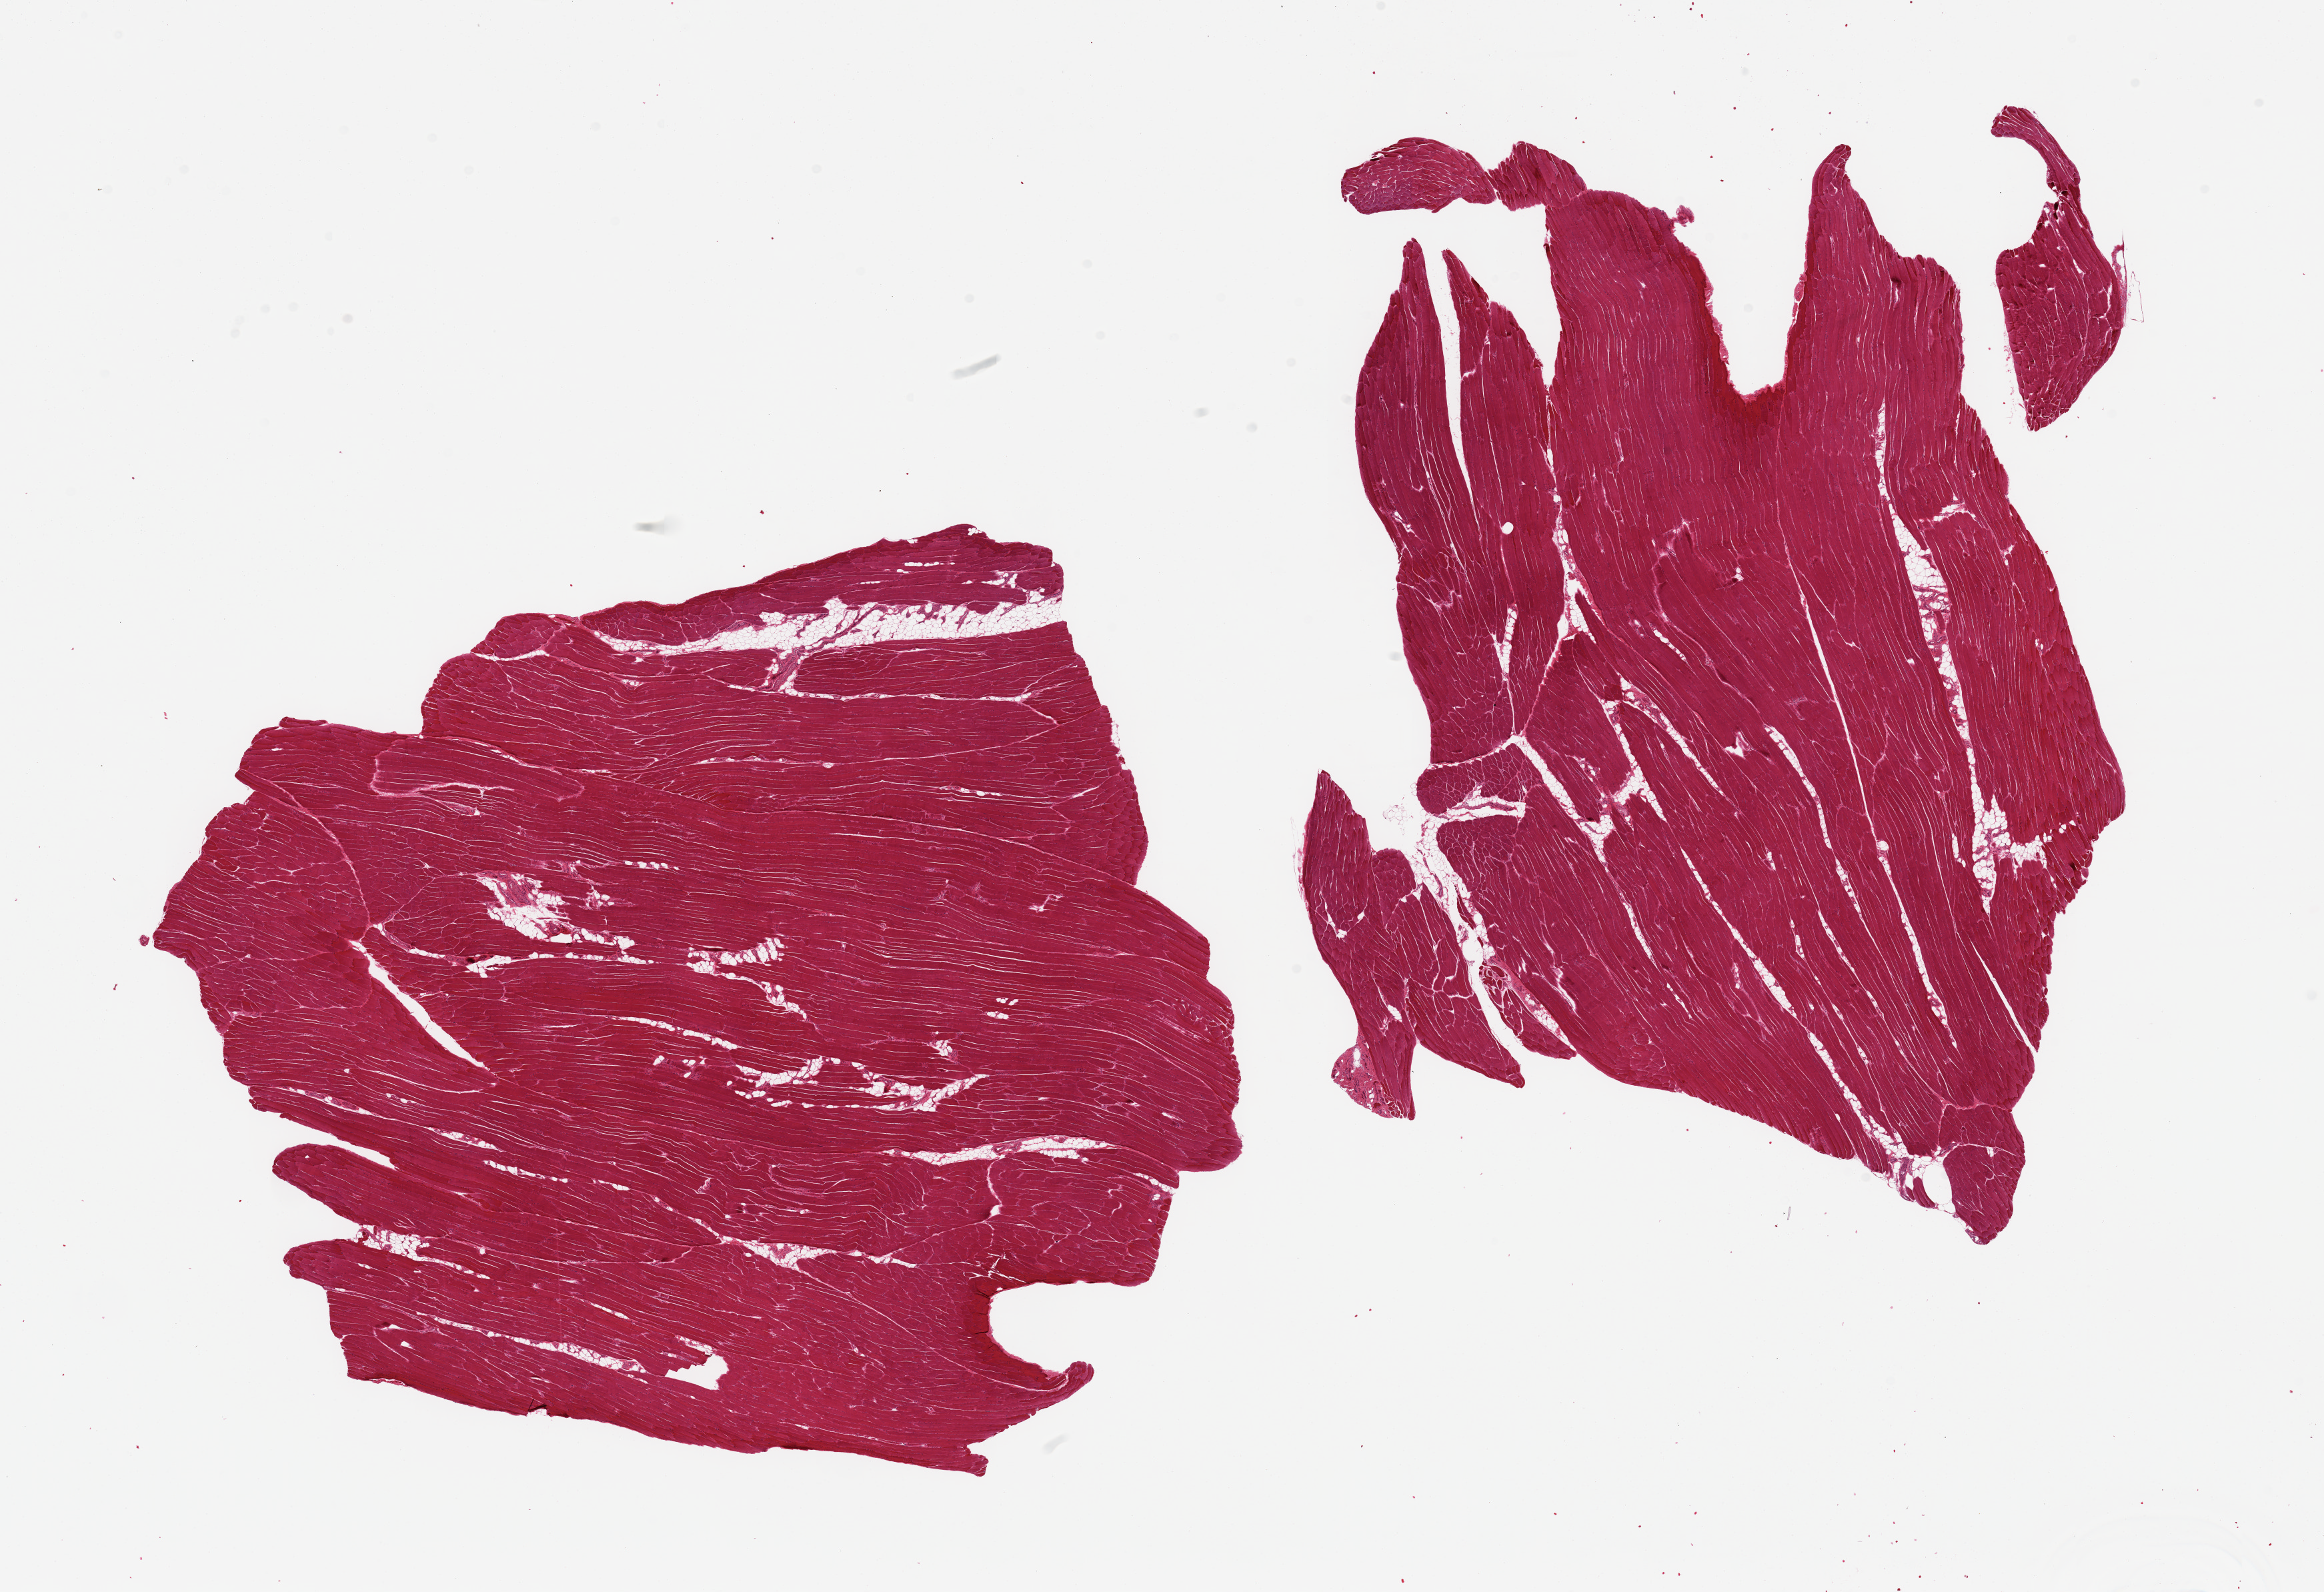
Whole-slide image, haematoxylin and eosin stain — shown as a low-resolution overview of the whole scanned area (about 27.6 x 18.9 mm), PAXgene-fixed paraffin-embedded (PFPE) section, target tissue: skeletal muscle, donor tissue sample. Donor: male.
- reviewer comment on this tissue sample: 2 pieces; 5% internal fat